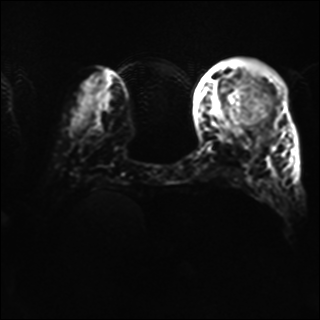
Breast MRI, one axial slice. Slice 14 of 40 in the series (ordered by position). Diffusion-weighted series; image 2 of 4 stored at this slice position (different b-values; order by instance number). 1.5 T. 4 mm slice thickness. 320 × 320 image matrix. Female patient.
Annotated regions visible in this slice (manually delineated by an expert):
- tumour on diffusion-weighted imaging: bounding box [x1, y1, x2, y2] px = [225, 87, 272, 128]